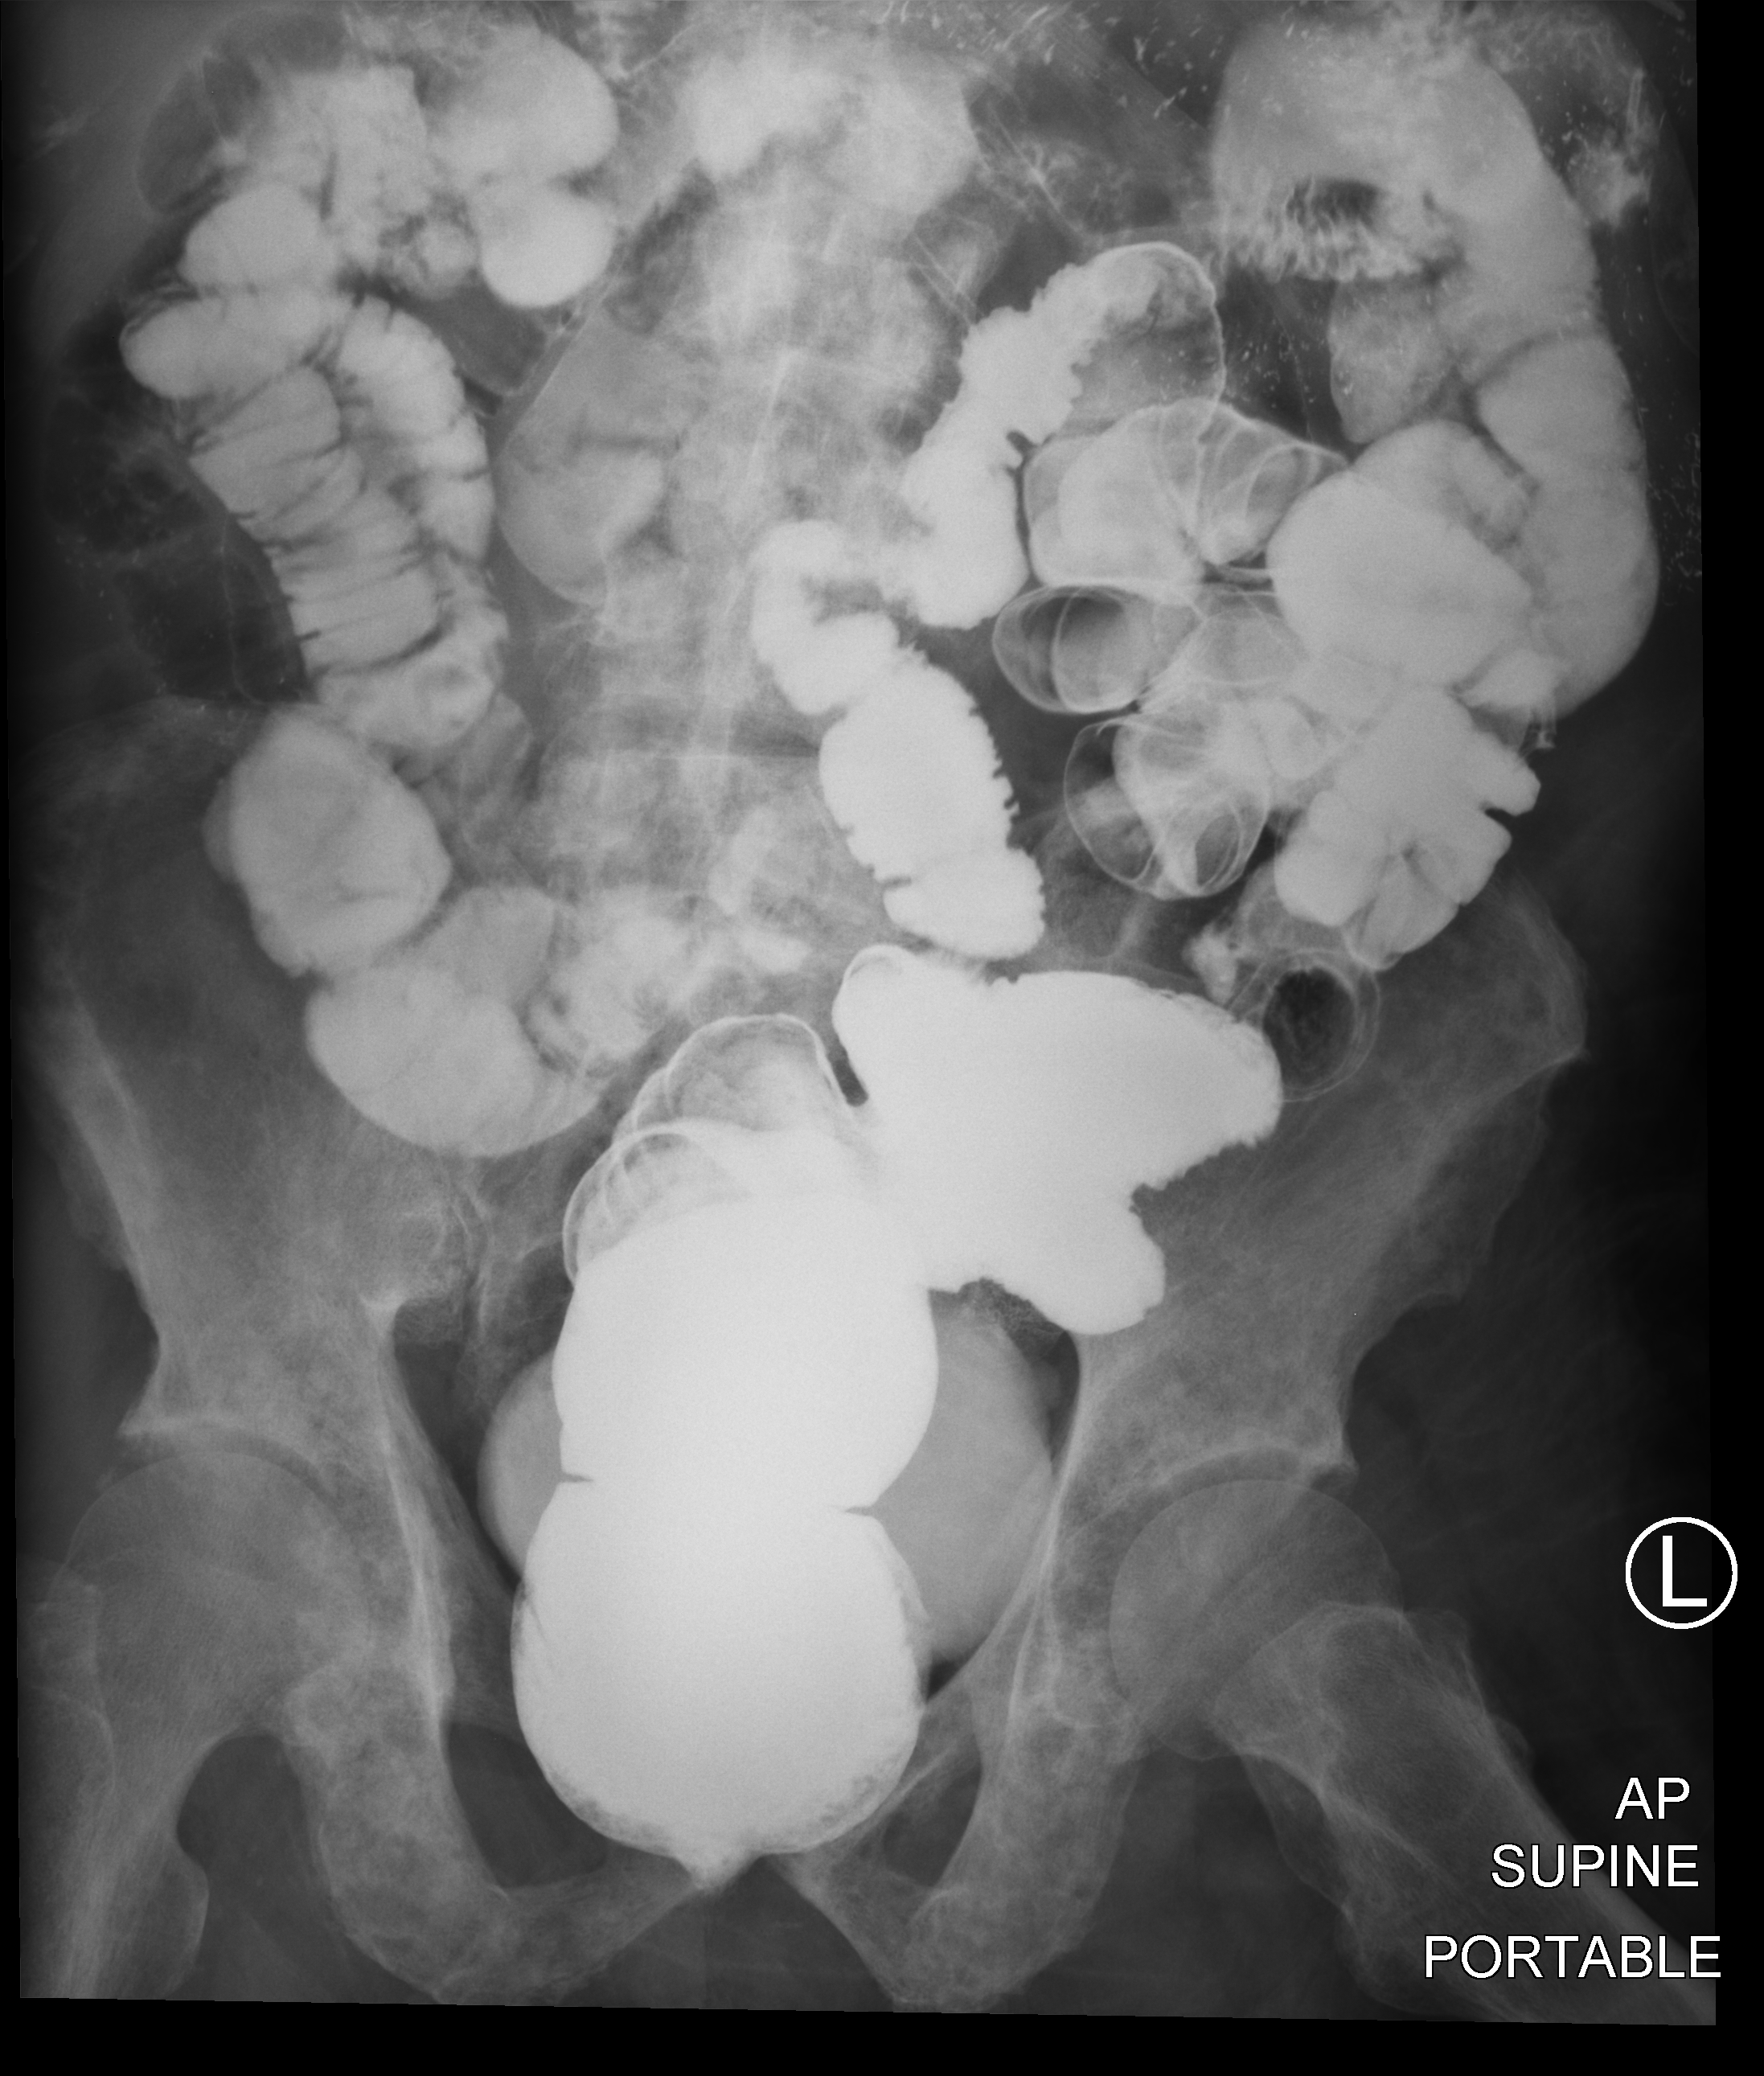
Bedside abdomen radiograph (computed radiography). Male patient hospitalised with COVID-19, age 75–90 years.
From the hospital-stay record, not from the radiograph (when in the stay this image was taken is not recorded):
- admitted to intensive care during this hospital stay: no
- length of hospital stay: 12 days